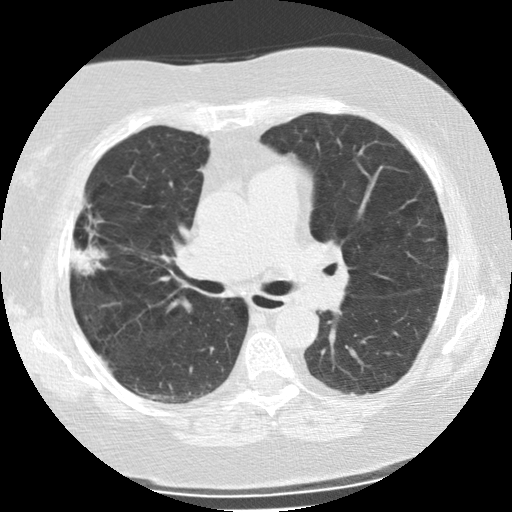
Axial slice from a low-dose chest CT screening exam. Second screening round (one year after baseline). Lung window (W 1500 / L -600 HU). 2.5 mm slice thickness. Female participant, aged 73 years at enrolment. Former smoker at enrolment.
- Expert reader's lesion annotation, bounding box (x1, y1, x2, y2) in pixels: (56, 206, 108, 280).
- The screening reader recorded 2 non-calcified nodules or masses ≥4 mm on this exam; which of them this box marks is not recorded.
- Later outcome: lung cancer diagnosed 47 days after this screen — bronchiolo-alveolar adenocarcinoma, NOS, right upper lobe, moderately differentiated (G2), stage IIIB (AJCC 6th edition), 21 mm at pathology.